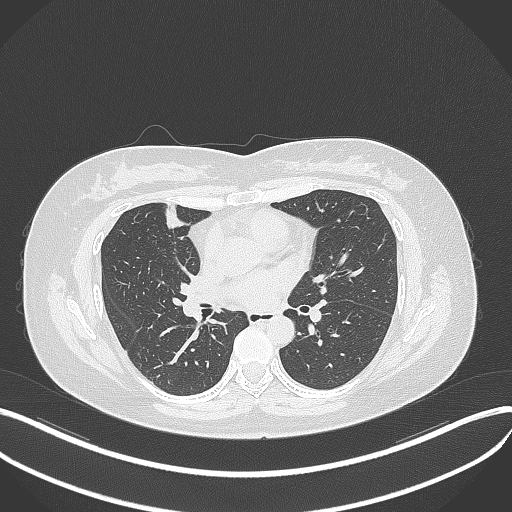
Chest CT, one axial slice. Position 163 of 273 along the scan axis. Reconstruction kernel B70f. 120 kVp. Lung window (W 1500 / L -600 HU). 1 mm slice thickness. 512 × 512 image matrix, field of view 400 × 400 mm. Patient: female, 42 years. Case-level facts recorded for this patient, not image findings: clinical TNM (as recorded): T1b N0 M0.
Annotated regions visible in this slice (rectangle marked by the reading radiologist):
- lung tumour (recorded histology: adenocarcinoma): bounding box (x1, y1, x2, y2) in pixels: (155, 202, 193, 236)